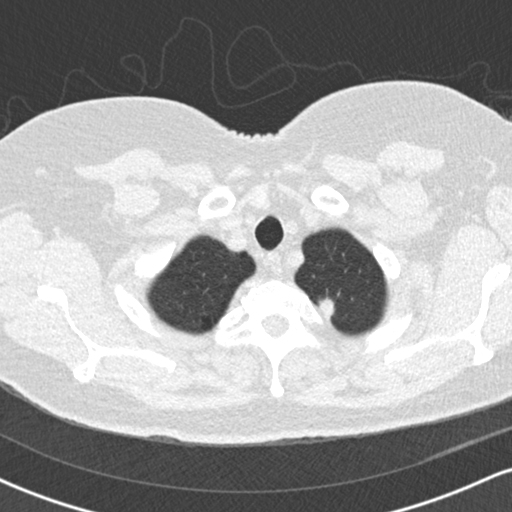
Low-dose screening chest CT, one axial slice. Slice 152 of 170 in the series (ordered by position). Reconstruction kernel B30f. 120 kVp. Lung window (W 1500 / L -600 HU). 2 mm slice thickness. 512 × 512 image matrix, field of view 320 × 320 mm.
Outlined on this slice (expert manual segmentation):
- lesion 1 (tumor, upper lobe of left lung): bounding box <320,299,334,319> (left, top, right, bottom; pixels)